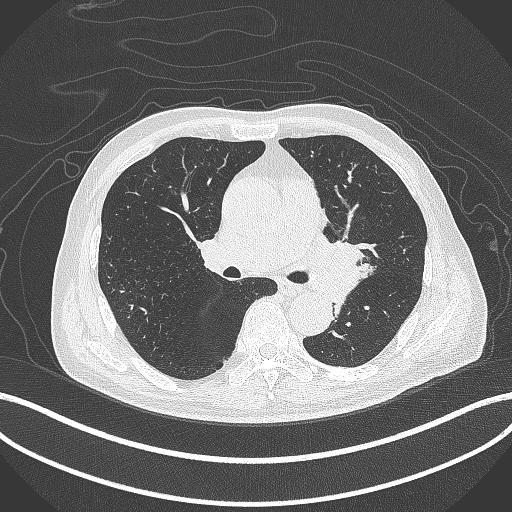
Chest CT, one axial slice; slice 252 of 417 in the series (ordered by position); reconstruction kernel B70f; 120 kVp; lung window (W 1500 / L -600 HU); 1 mm slice thickness; 512 × 512 image matrix, field of view 400 × 400 mm. Patient: male, 77 years. From the clinical record (not read from this slice): clinical TNM (as recorded): T3 N1 M0.
Annotated regions visible in this slice (bounding box drawn by a radiologist):
- lung tumour (recorded histology: adenocarcinoma): box from (x=307, y=222) to (x=371, y=301) px